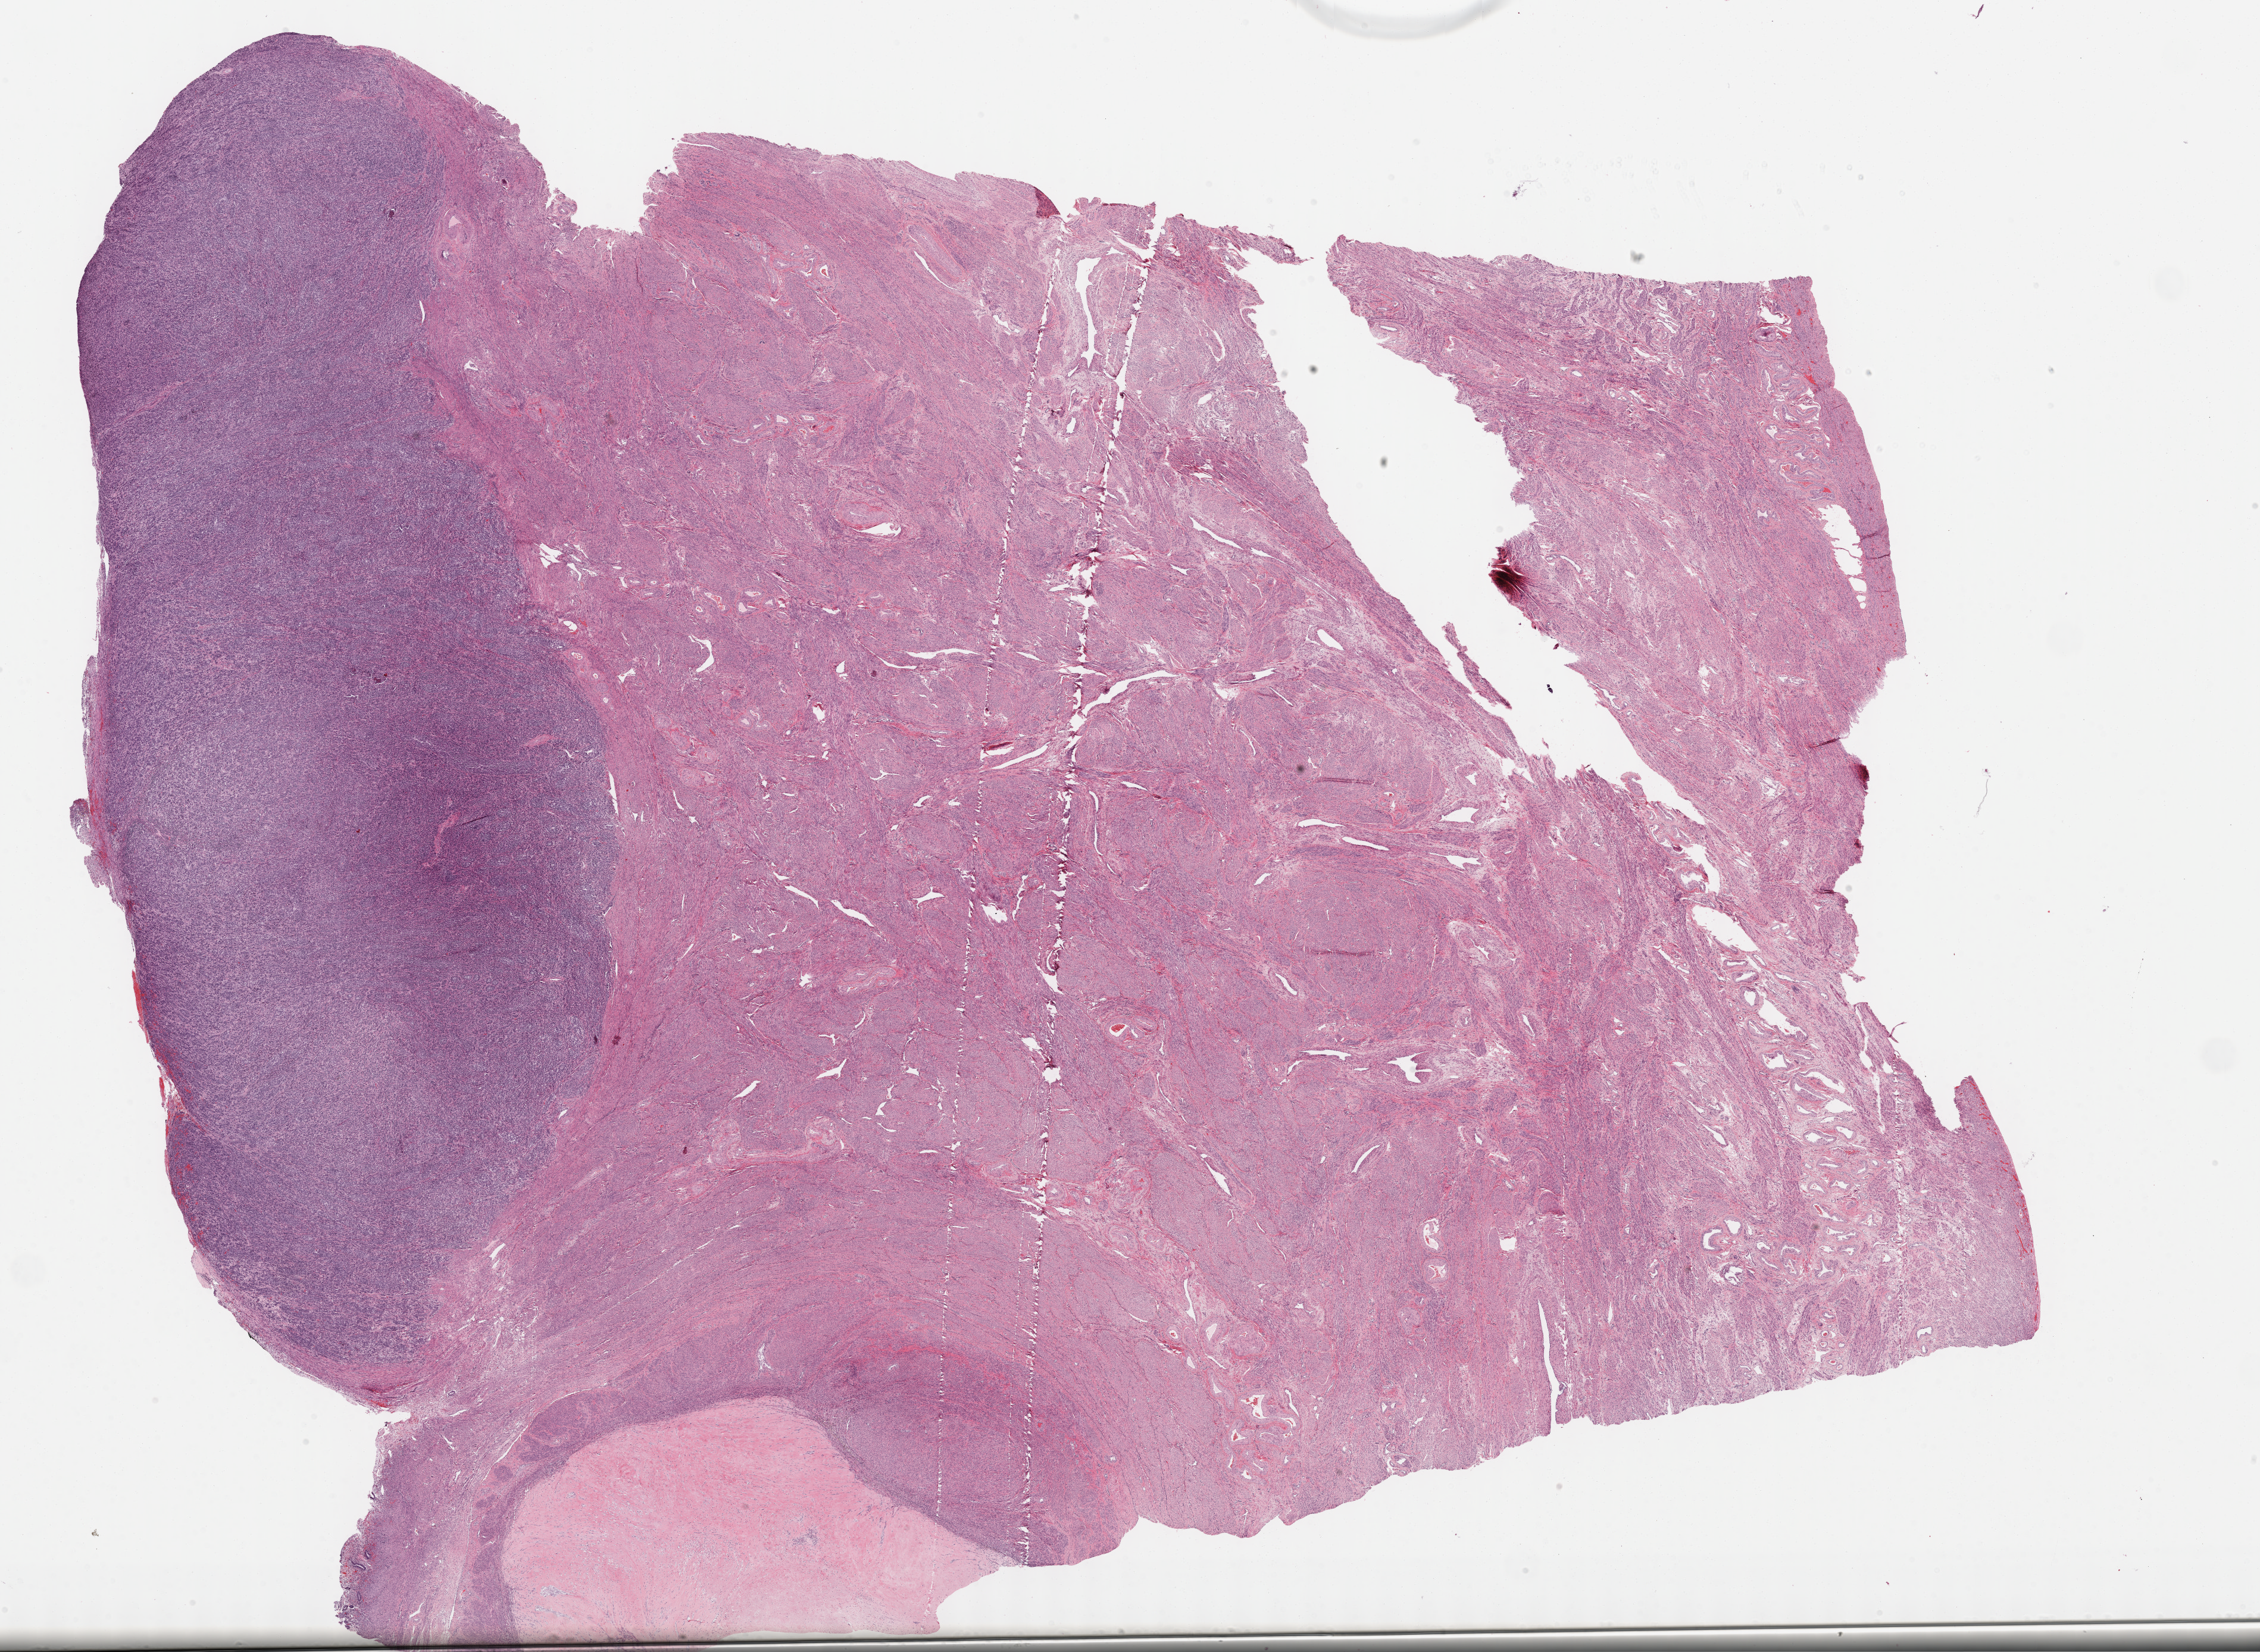
Digitized H&E-stained tissue section (whole slide), whole scanned area (about 30.7 x 22.4 mm) shown as a low-resolution overview, formalin-fixed paraffin-embedded (FFPE) diagnostic section, skin, primary tumour sample. Patient sex: female.
- diagnosis: Malignant melanoma, NOS